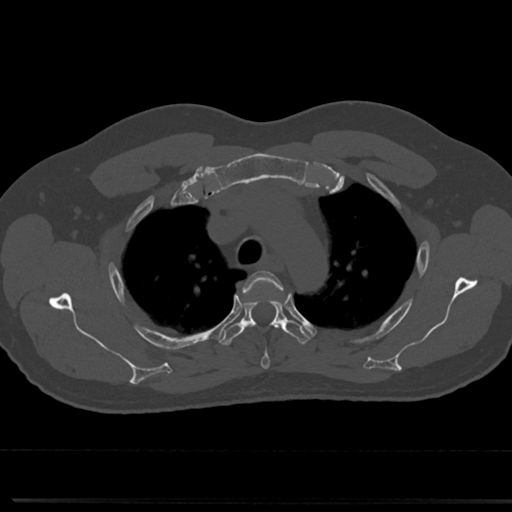
CT including the spine, one axial slice; position 565 of 817 along the scan axis; reconstruction kernel Br40s/3; 120 kVp; bone window (W 1800 / L 400 HU); 512 × 512 image matrix, field of view 355 × 355 mm. Patient: male, 61 years. From the clinical record (not read from this slice): primary cancer: prostate.
Structures marked on this image (semi-automatically segmented with operator editing):
- T3 vertebra: box from (x=244, y=270) to (x=291, y=369) px
- T4 vertebra: (x=219, y=299)–(x=311, y=346)